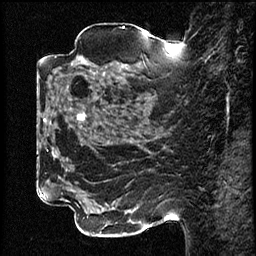
Breast MRI (dynamic contrast-enhanced), one sagittal slice; dynamic contrast-enhanced study with each time point stored as its own series, time point 2 of 3 at this slice position (early post-contrast, ordered by acquisition time); 1.5 T; TE 4.2 ms, TR 17.6 ms; 2 mm slice thickness; 256 × 256 image matrix, field of view 200 × 200 mm. Patient: female, 42 years. Case-level facts recorded for this patient, not image findings: setting: breast cancer imaged before/during neoadjuvant chemotherapy; receptor status: HER2-positive.
Structures marked on this image (semi-automatic segmentation, software-assisted and operator-edited):
- analysis volume of interest (the breast-tissue region the enhancement analysis was run in; not a lesion): box from (x=50, y=48) to (x=131, y=129) px
- tumour enhancement mask (voxels above the 100 % enhancement threshold inside the analysis volume of interest): (x=77, y=113)–(x=85, y=120)